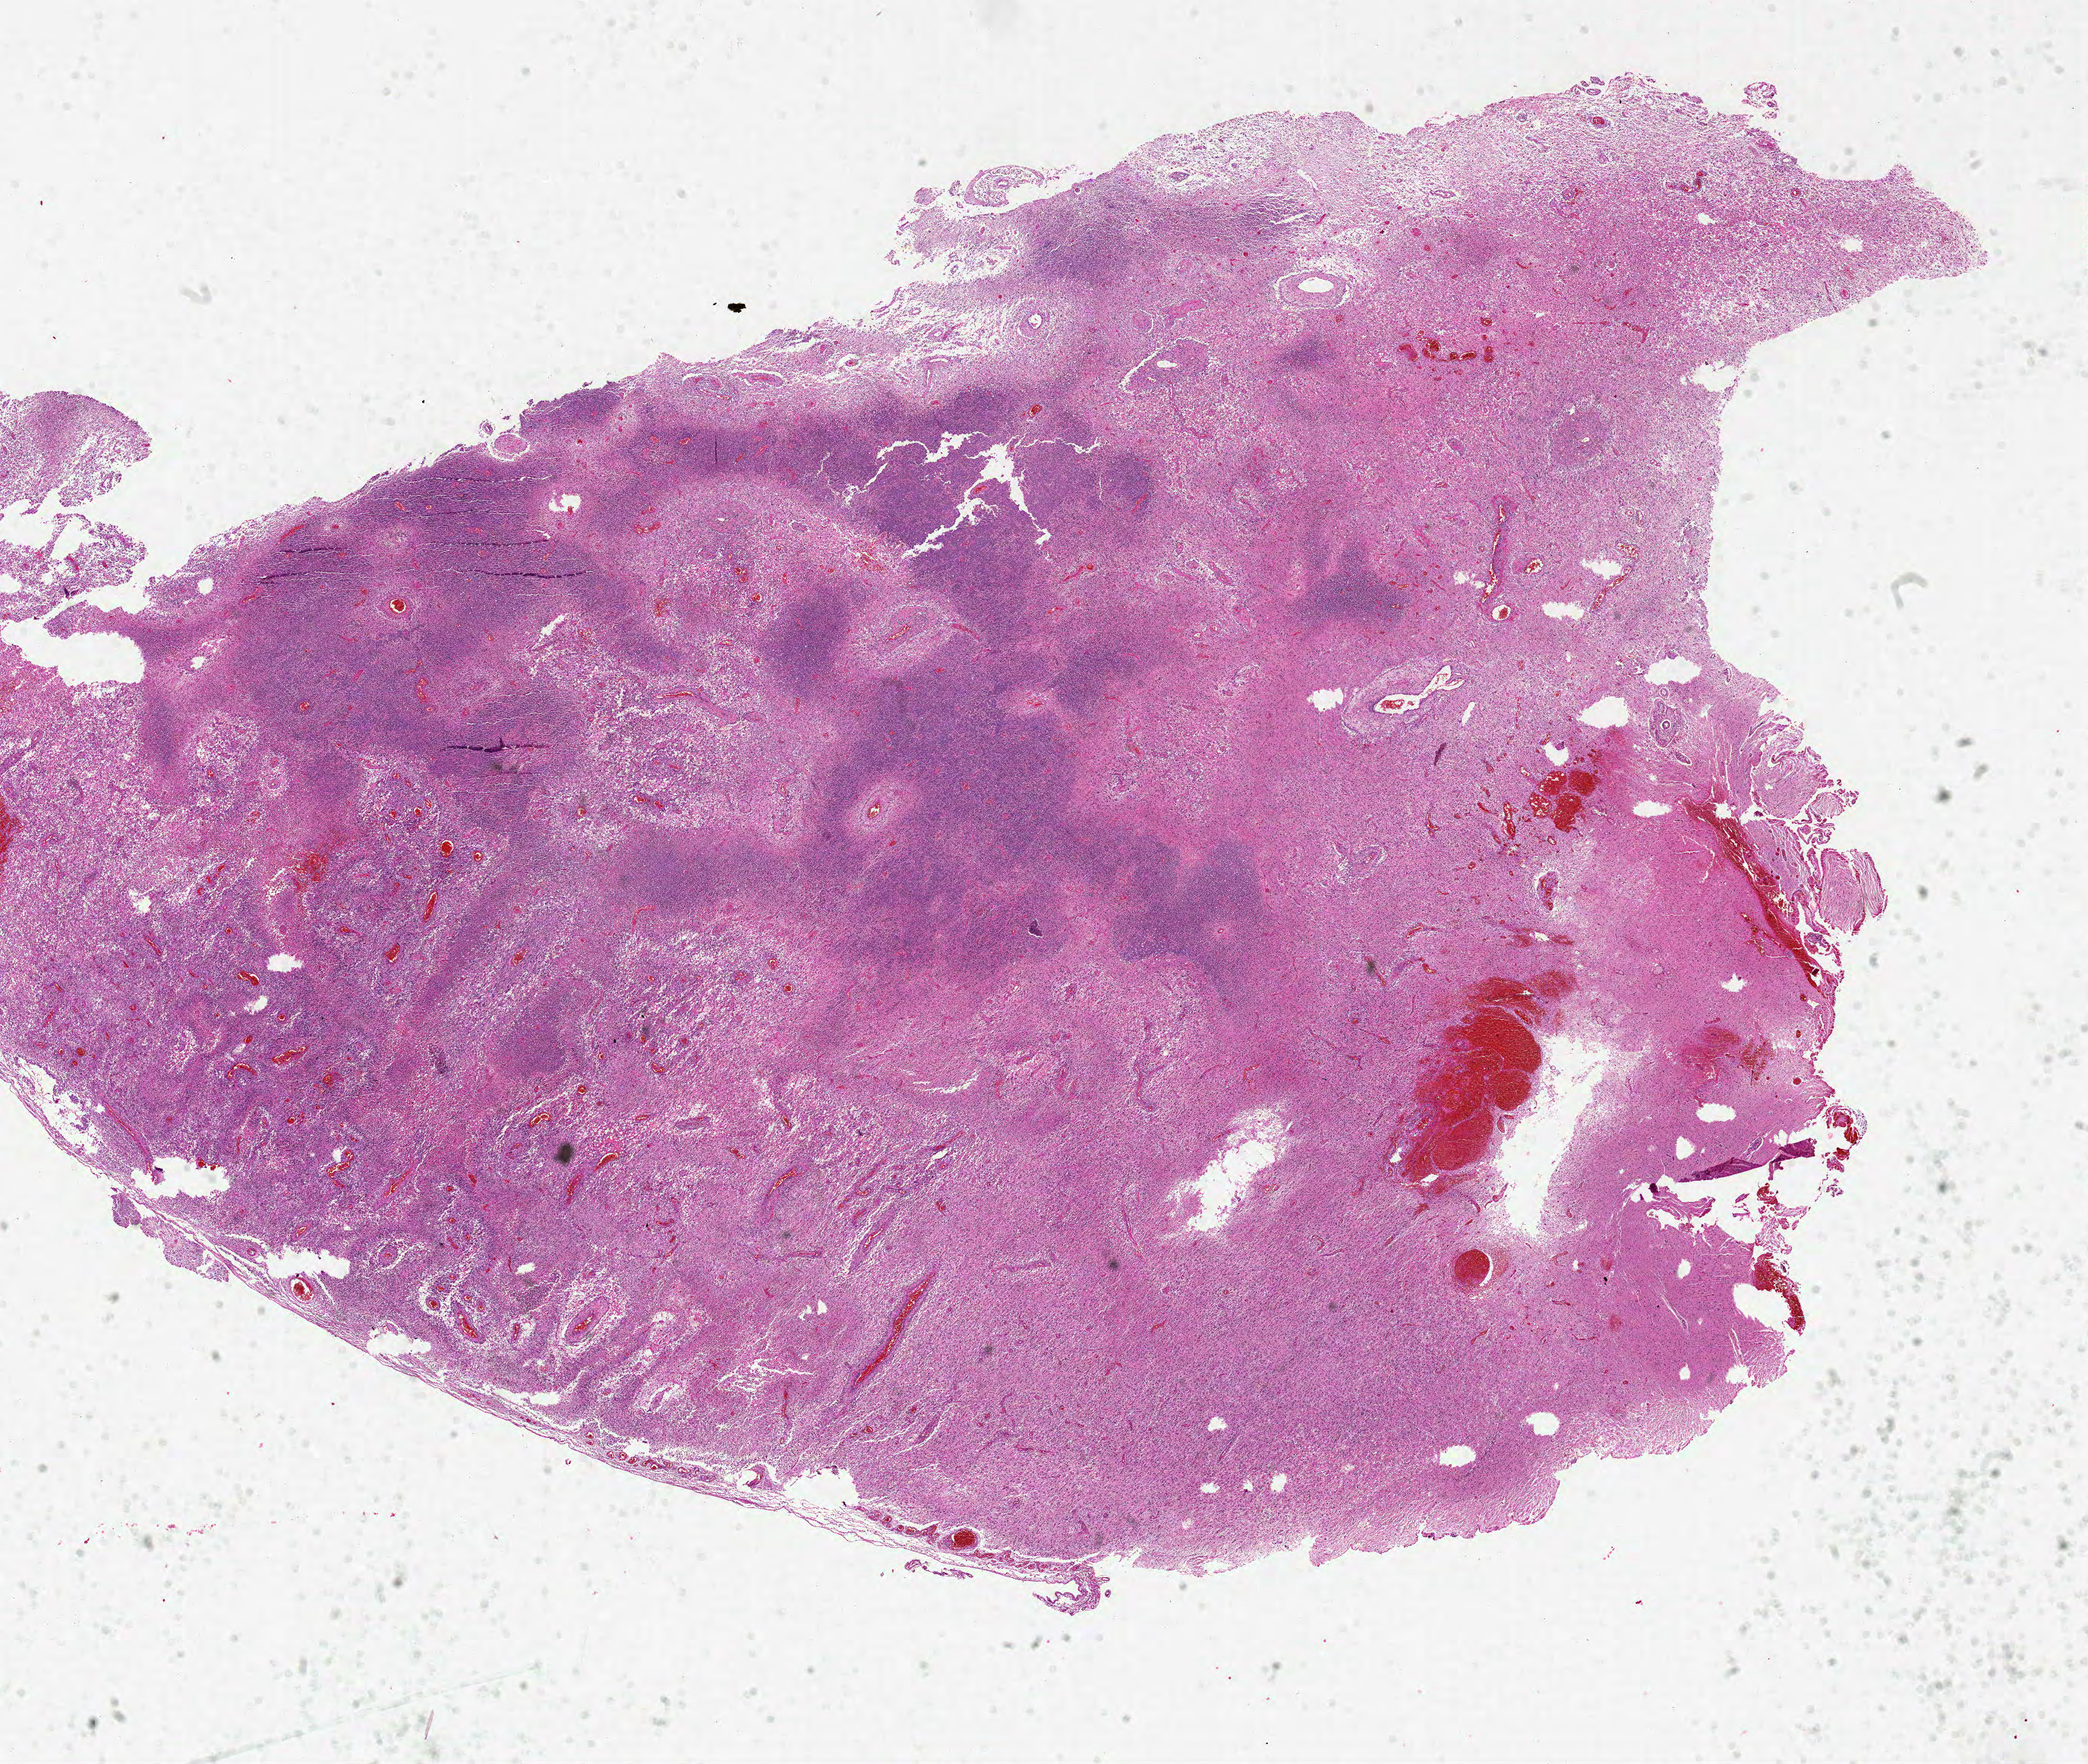
Digitized Hematoxylin and eosin (H&E) stained tissue section (whole slide), a low-resolution overview of the entire scanned area, about 22.0 x 18.6 mm. Formalin-fixed paraffin-embedded (FFPE) diagnostic section. Primary tumour sample from the brain. Patient: female, age at initial diagnosis 75 years.
• pathologic diagnosis: Glioblastoma